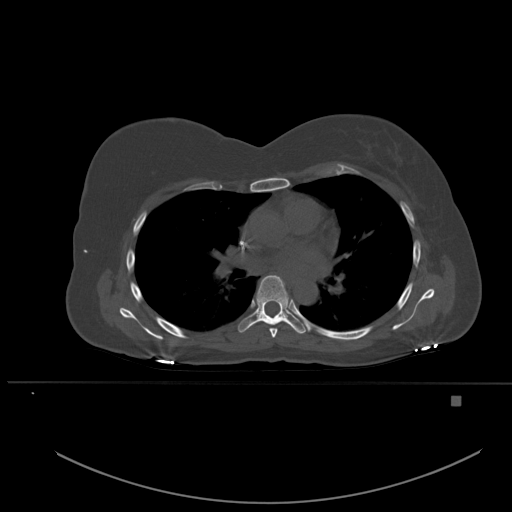
CT including the spine, one axial slice. Position 354 of 651 along the scan axis. Bone window (W 1800 / L 400 HU). 1.5 mm slice thickness. 512 × 512 image matrix, field of view 443 × 443 mm. Female patient, age 49 years. Case-level facts recorded for this patient, not image findings: primary cancer: breast; vertebrae with lytic lesions (as recorded): L3, T12, L4.
Outlined on this slice (semi-automatically segmented with operator editing):
- T5 vertebra: bounding box [x1, y1, x2, y2] px = [269, 328, 278, 338]
- T6 vertebra: [238, 275, 306, 334]